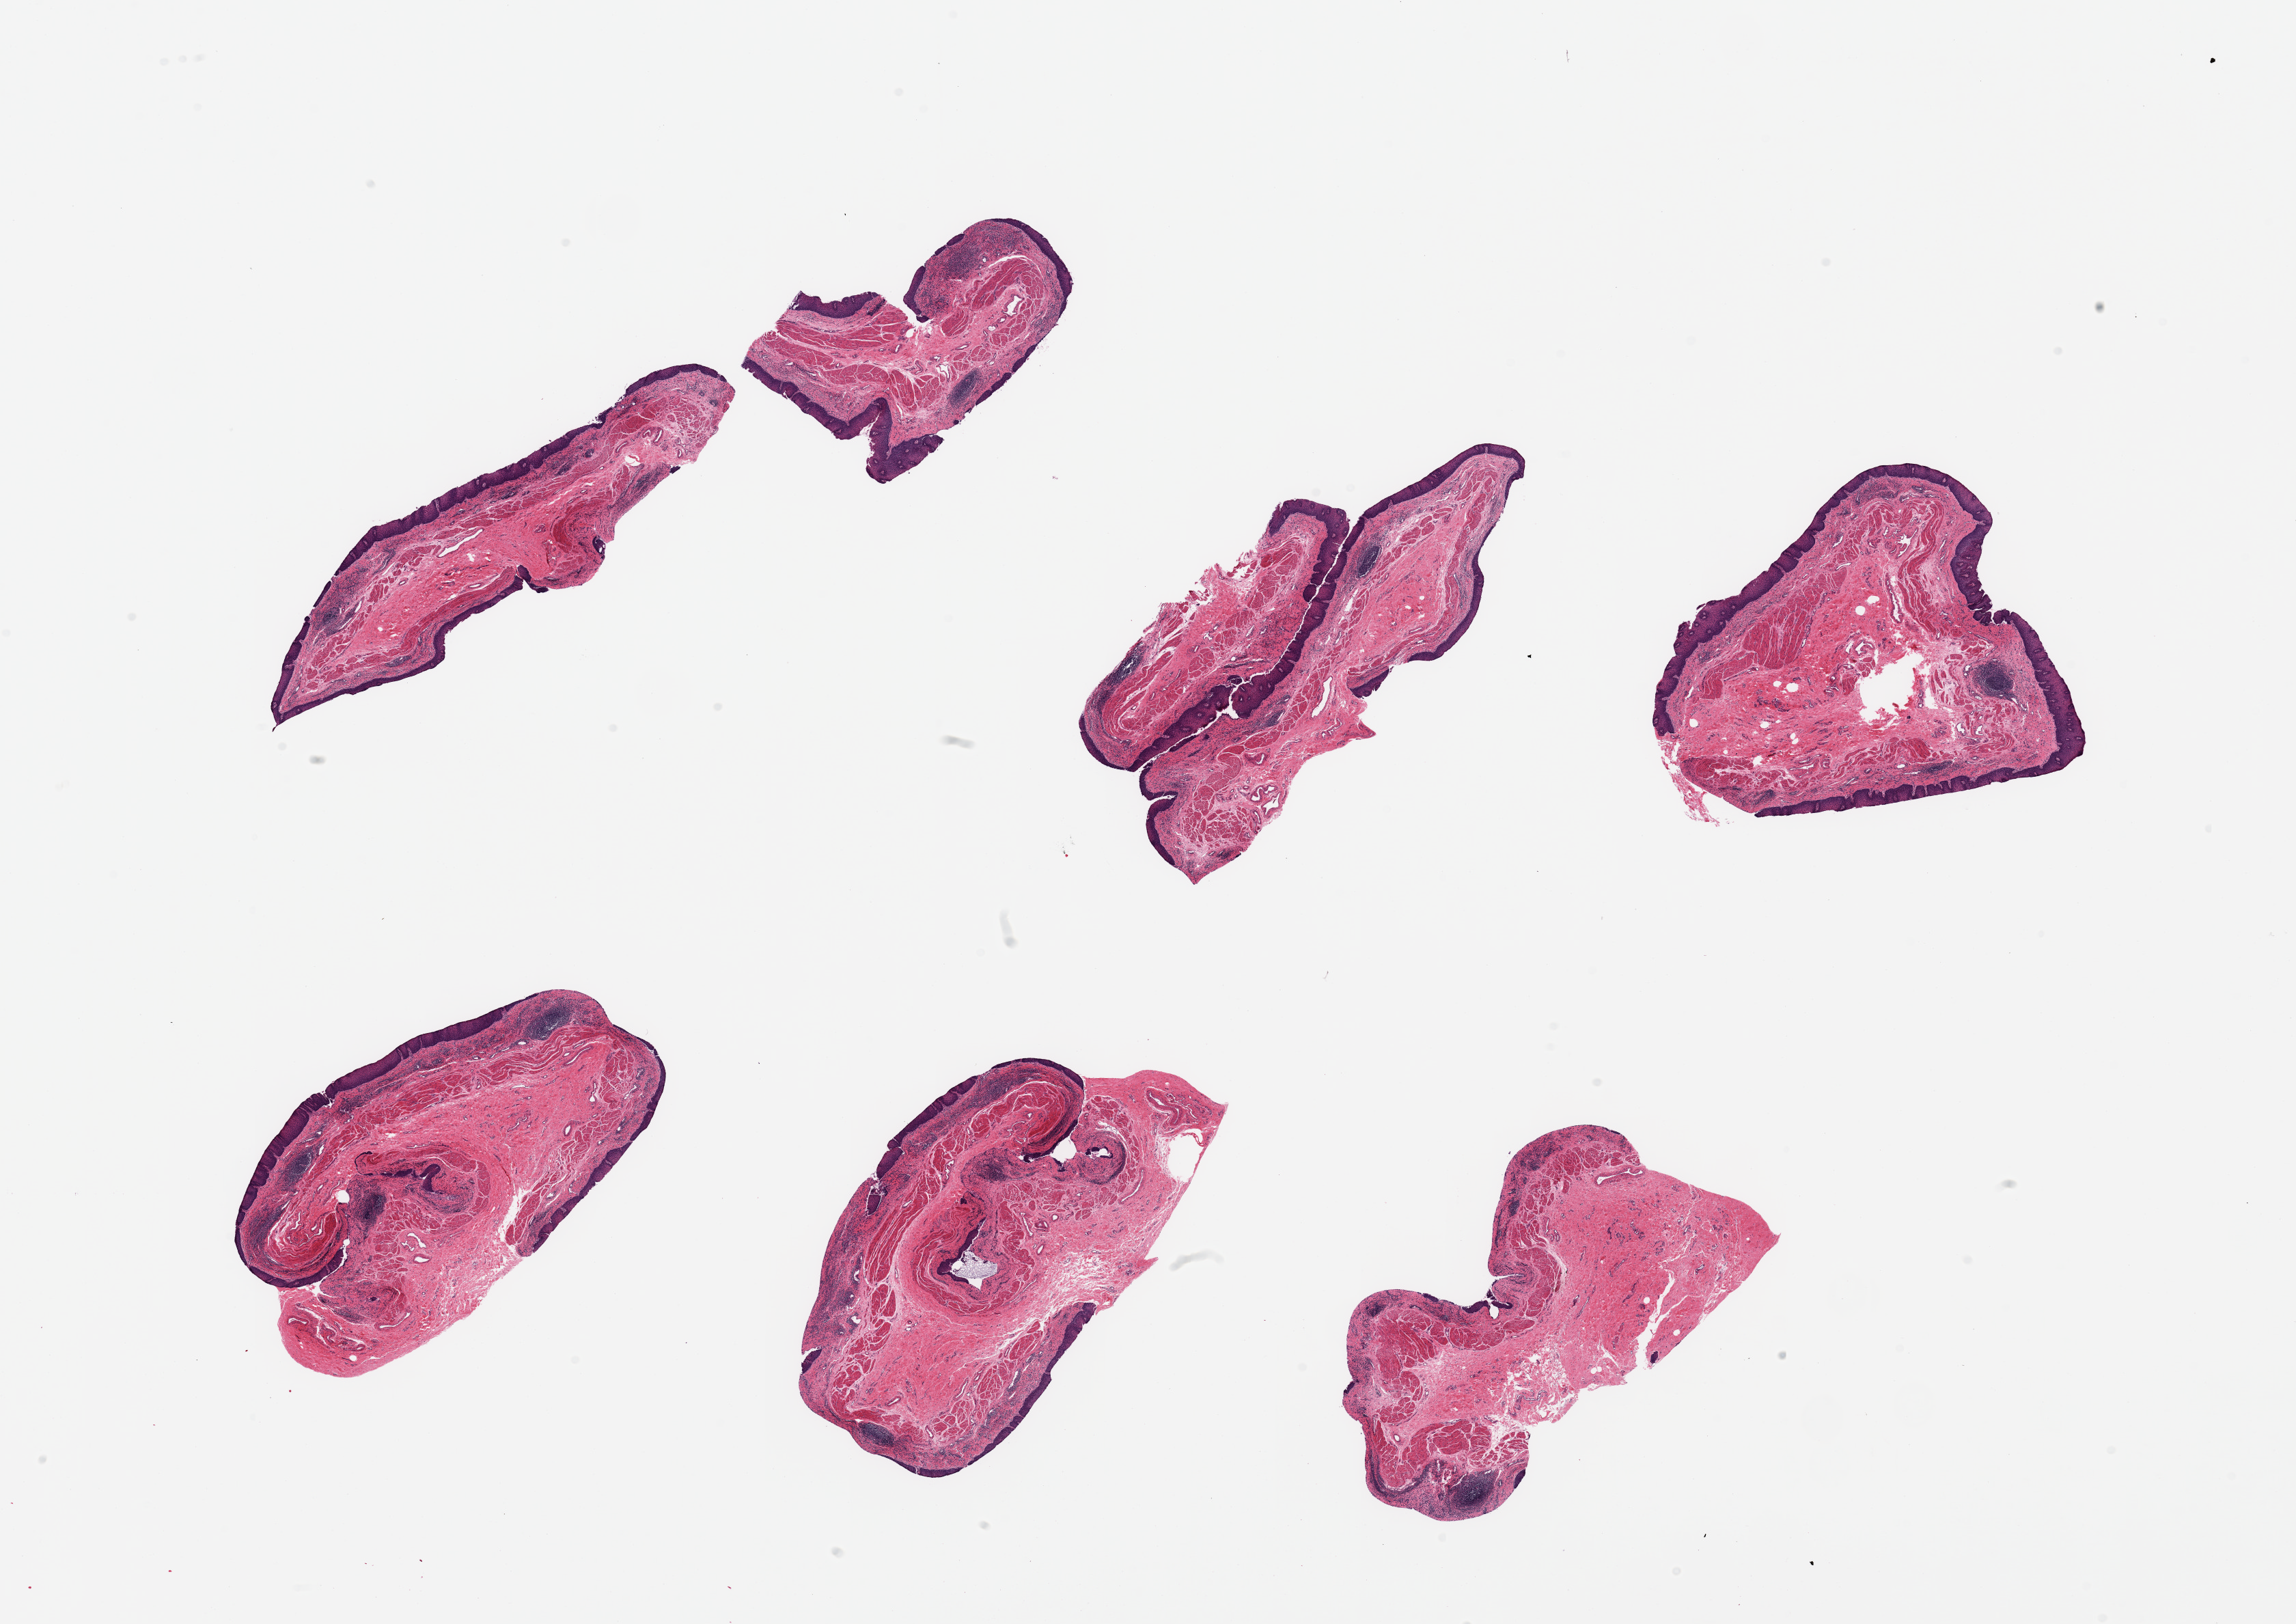
Whole-slide image, haematoxylin and eosin stain, brightfield — shown as a low-resolution overview of the whole scanned area (about 26.6 x 18.8 mm), PAXgene-fixed paraffin-embedded (PFPE) section, target tissue: esophageal mucous membrane, tissue donor sample. Donor sex: male.
Pathologist's review note for this sample: 6 pieces, squamous mucosa up to ~0.2mm, ~20% thickness.